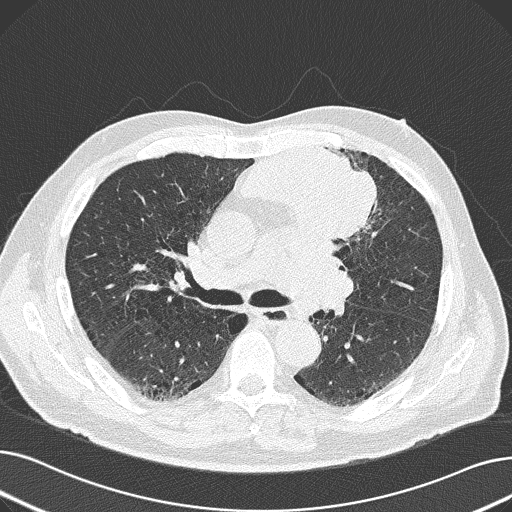
Chest CT (low-dose screening protocol), one axial image; first (baseline) screen; lung window (W 1500 / L -600 HU); 2 mm slice thickness; lung (sharp) reconstruction kernel (B50f); slice 73 of 165 in the series; 512 × 512 image matrix, field of view 370 × 370 mm. Male, age 69 years at enrolment.
Lesion marked by an expert reader, bounding box <235,134,384,250> (left, top, right, bottom; pixels). Screening reader's record for this exam (one nodule recorded; not confirmed to be the boxed lesion): non-calcified nodule or mass ≥4 mm, left upper lobe, 6 × 10 mm, spiculated (stellate) margins, soft tissue attenuation.